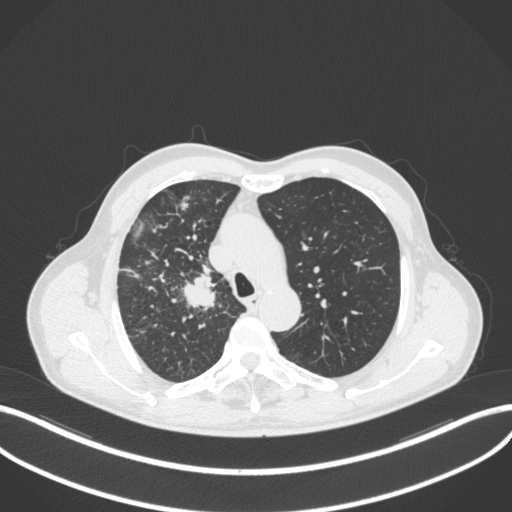
Chest CT, one axial slice; position 352 of 490 along the scan axis; reconstruction kernel B31f; lung window (W 1500 / L -600 HU); 512 × 512 image matrix. Patient: male, 69 years. From the clinical record (not read from this slice): clinical TNM (as recorded): T2a N0 M0.
Structures marked on this image (rectangle marked by the reading radiologist):
- lung tumour (recorded histology: adenocarcinoma): bounding box <180,269,225,314> (left, top, right, bottom; pixels)